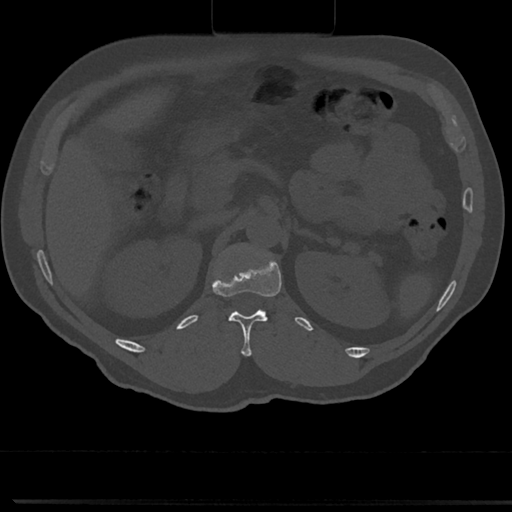
CT including the spine, one axial slice; position 128 of 817 along the scan axis; reconstruction kernel Br40s/3; 120 kVp; bone window (W 1800 / L 400 HU); 0.5 mm slice thickness; 512 × 512 image matrix, field of view 355 × 355 mm. Patient: male, 61 years. From the clinical record (not read from this slice): primary cancer: prostate.
Outlined on this slice (semi-automatically segmented with operator editing):
- L1 vertebra: bounding box [x1, y1, x2, y2] px = [212, 242, 270, 317]
- T12 vertebra: [226, 273, 282, 356]